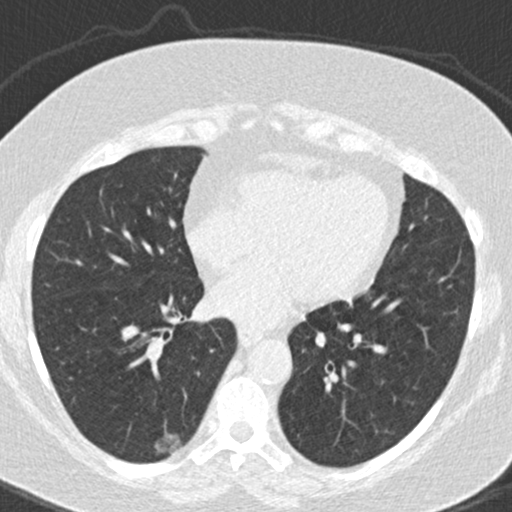
Low-dose screening chest CT, one axial slice; slice 72 of 177 in the series (ordered by position); reconstruction kernel B30f; 120 kVp; lung window (W 1500 / L -600 HU); 512 × 512 image matrix.
Annotated regions visible in this slice (manually delineated by an expert):
- lesion 1 (tumor, lower lobe of right lung): box from (x=154, y=433) to (x=182, y=452) px